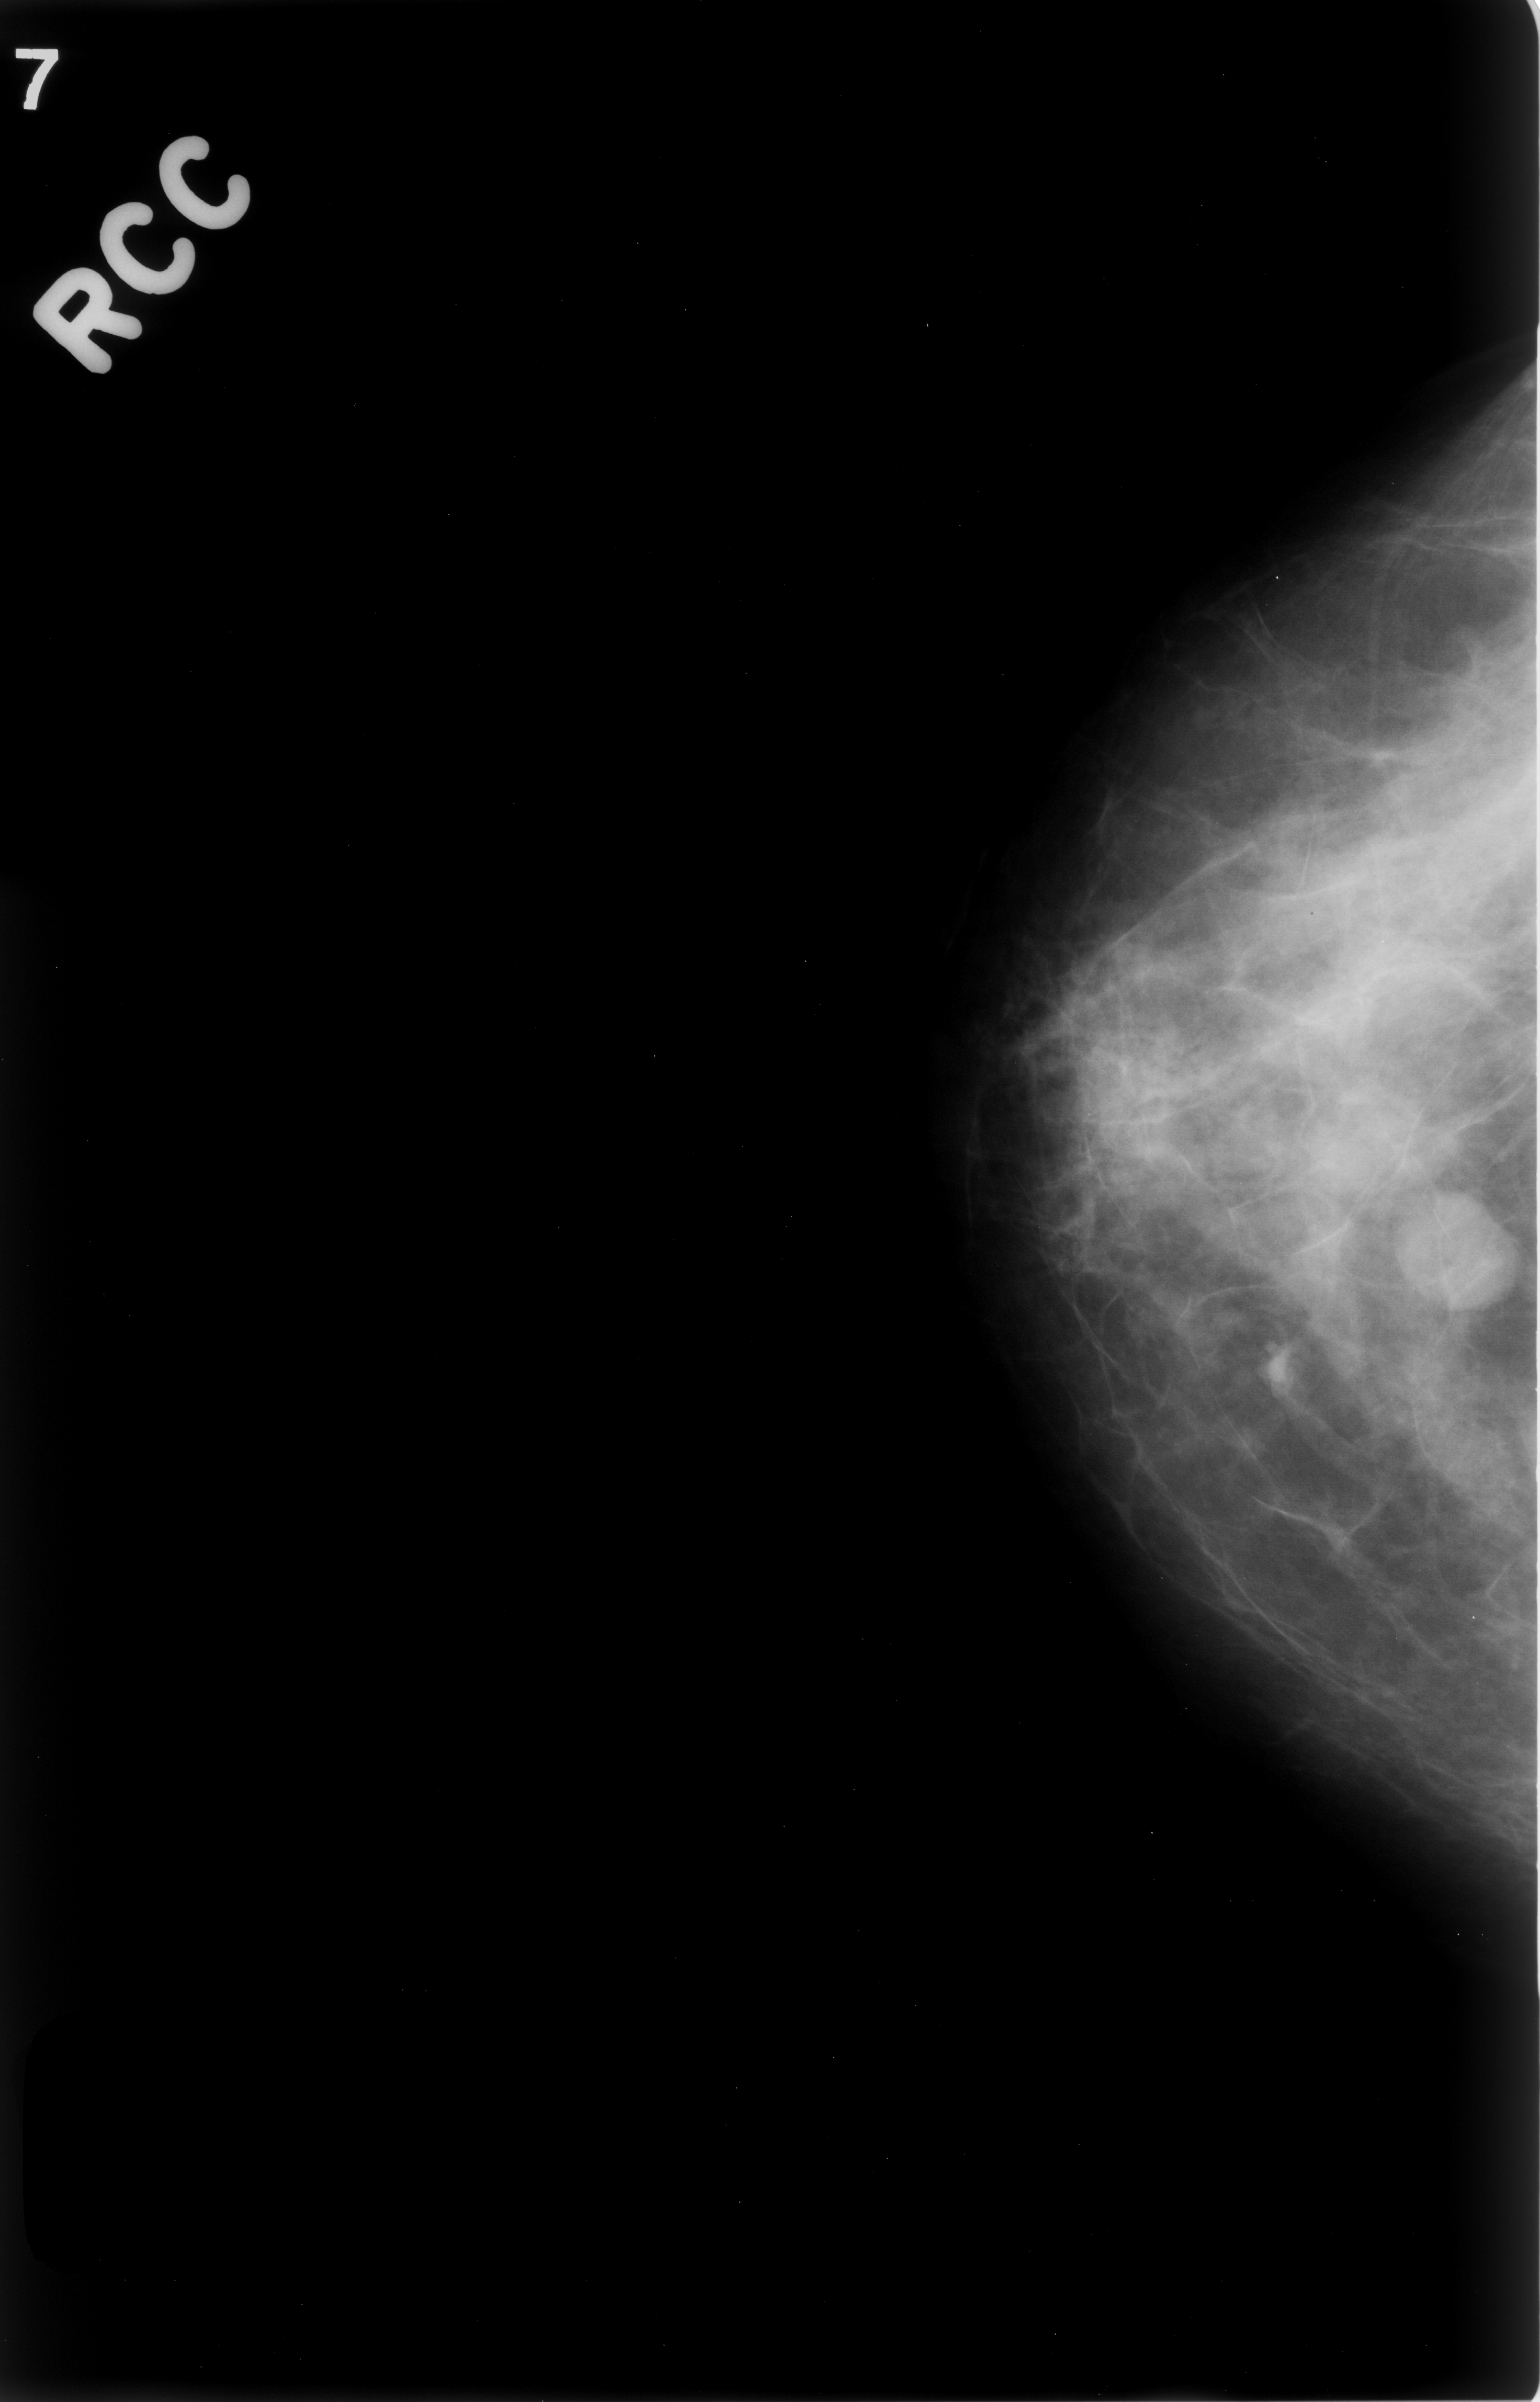
Scanned film-screen mammogram. Right breast. CC view. Breast composition: scattered fibroglandular densities (BI-RADS density category 2 of 4). 1540 × 2402 image matrix.
Marked abnormalities (boxes around the expert regions of interest):
- mass, shape oval, margins circumscribed; BI-RADS assessment category 3; pathology (as recorded): benign: bounding box [x1, y1, x2, y2] px = [1389, 1168, 1540, 1342]